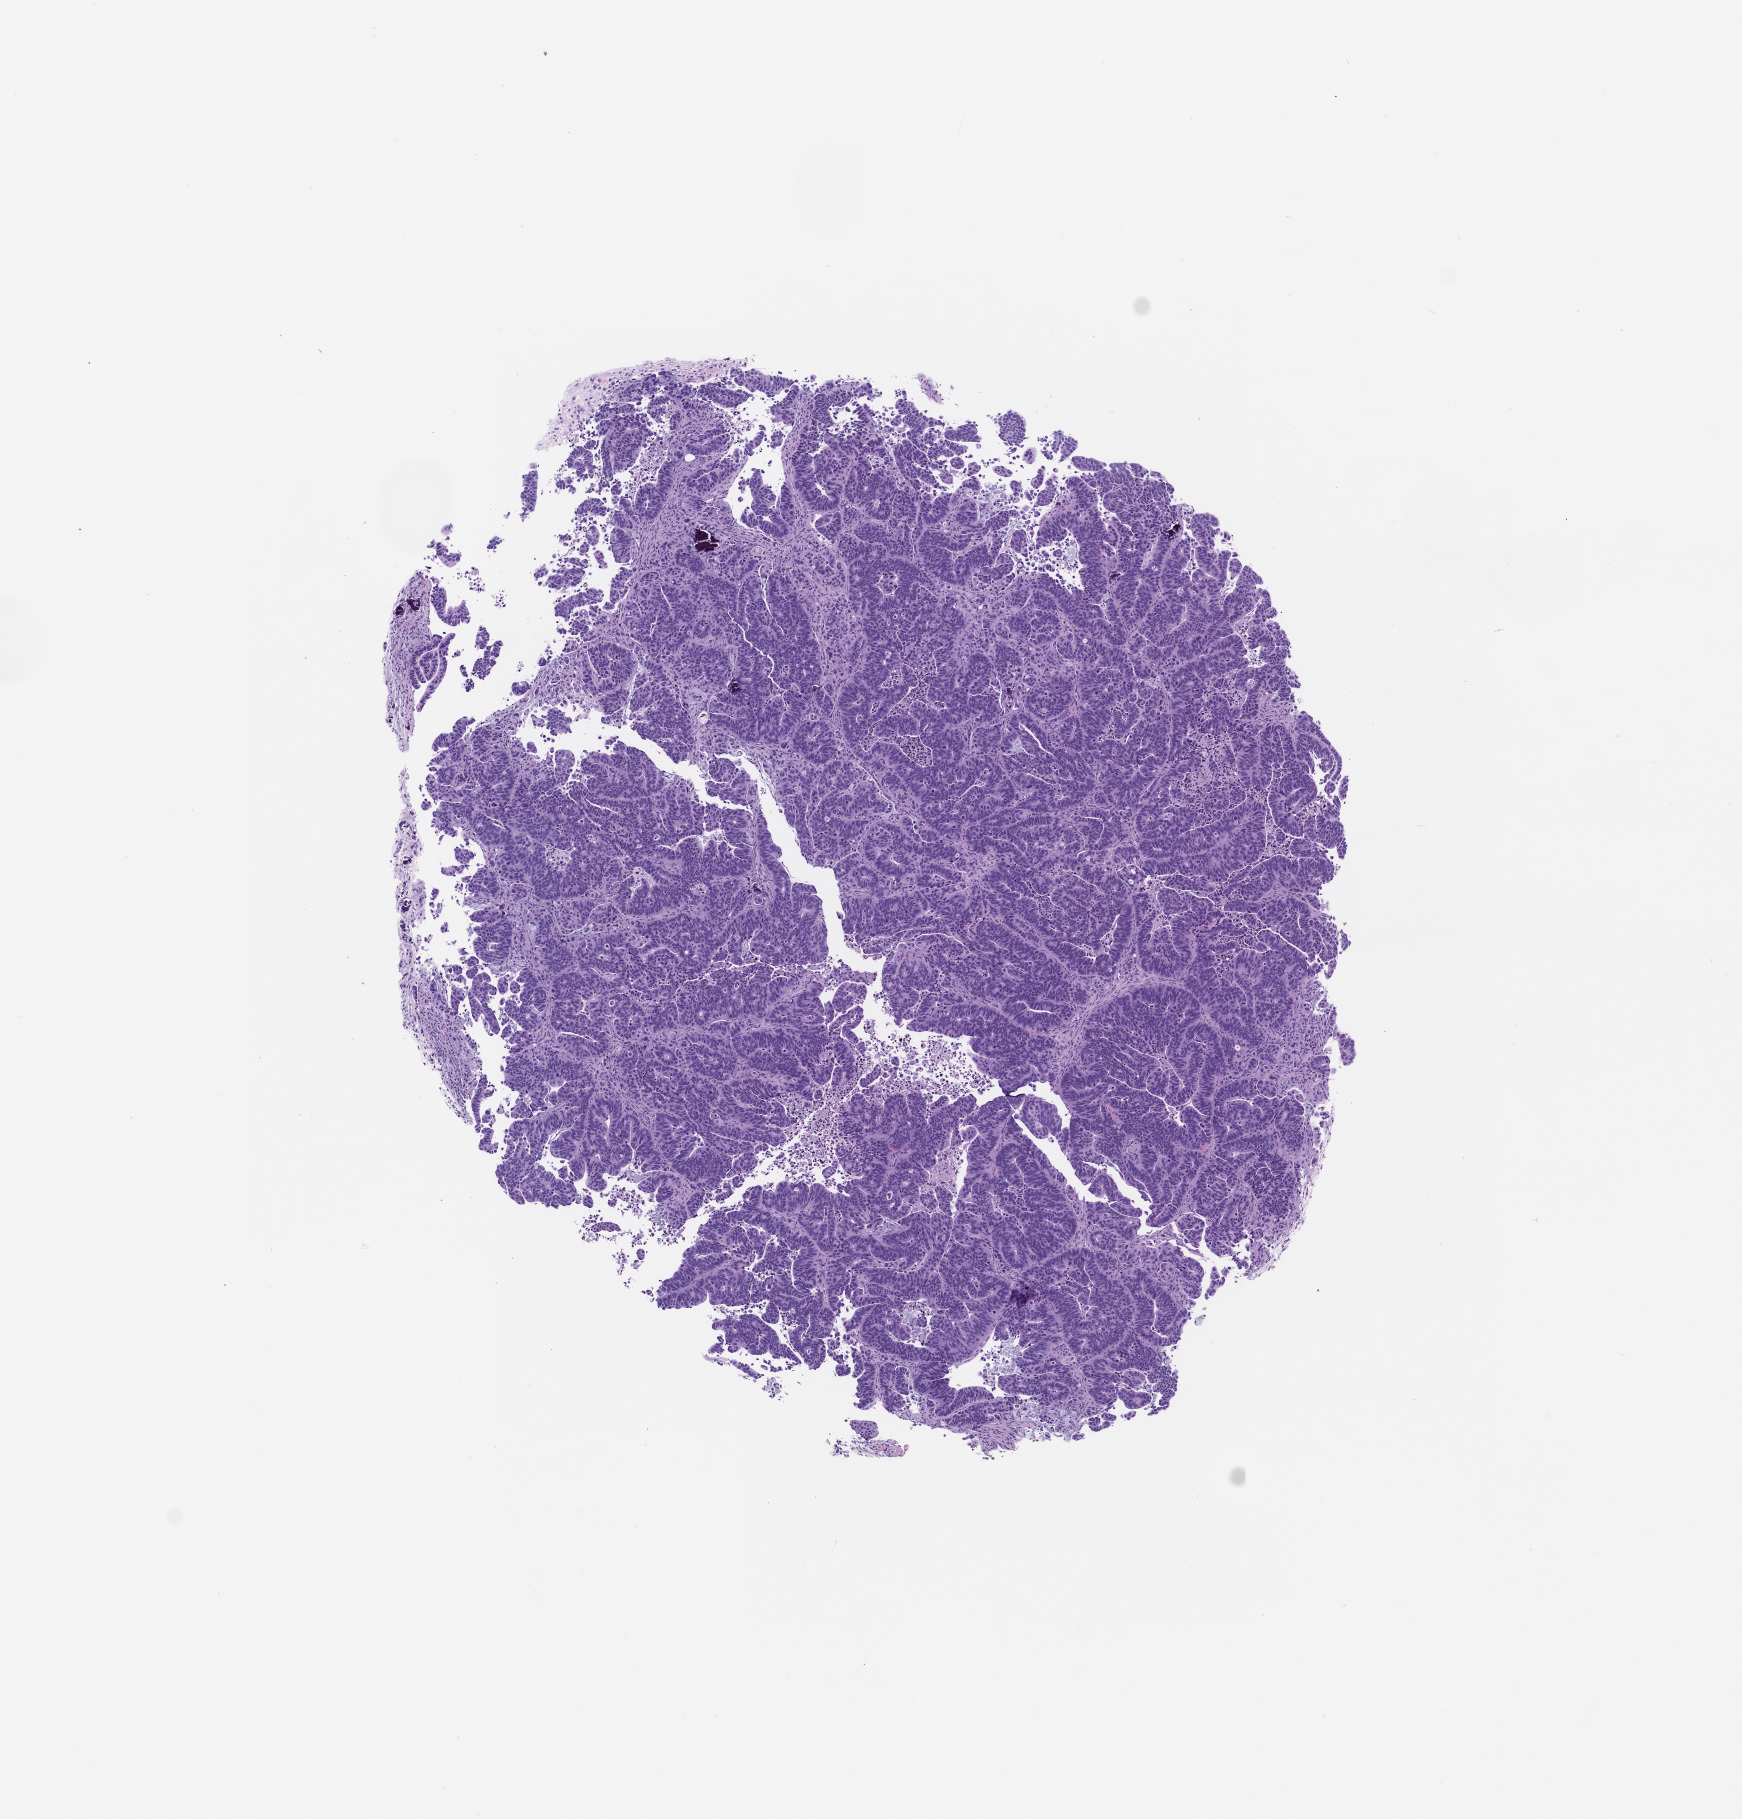
Whole-slide image, H&E: patient-derived xenograft (human tumor grown in a mouse), passage 1, a low-resolution overview of the entire scanned area, about 7.0 x 7.3 mm, formalin-fixed paraffin-embedded section, tumor site category: colon.
Originating patient diagnosis: Colon Adenocarcinoma.